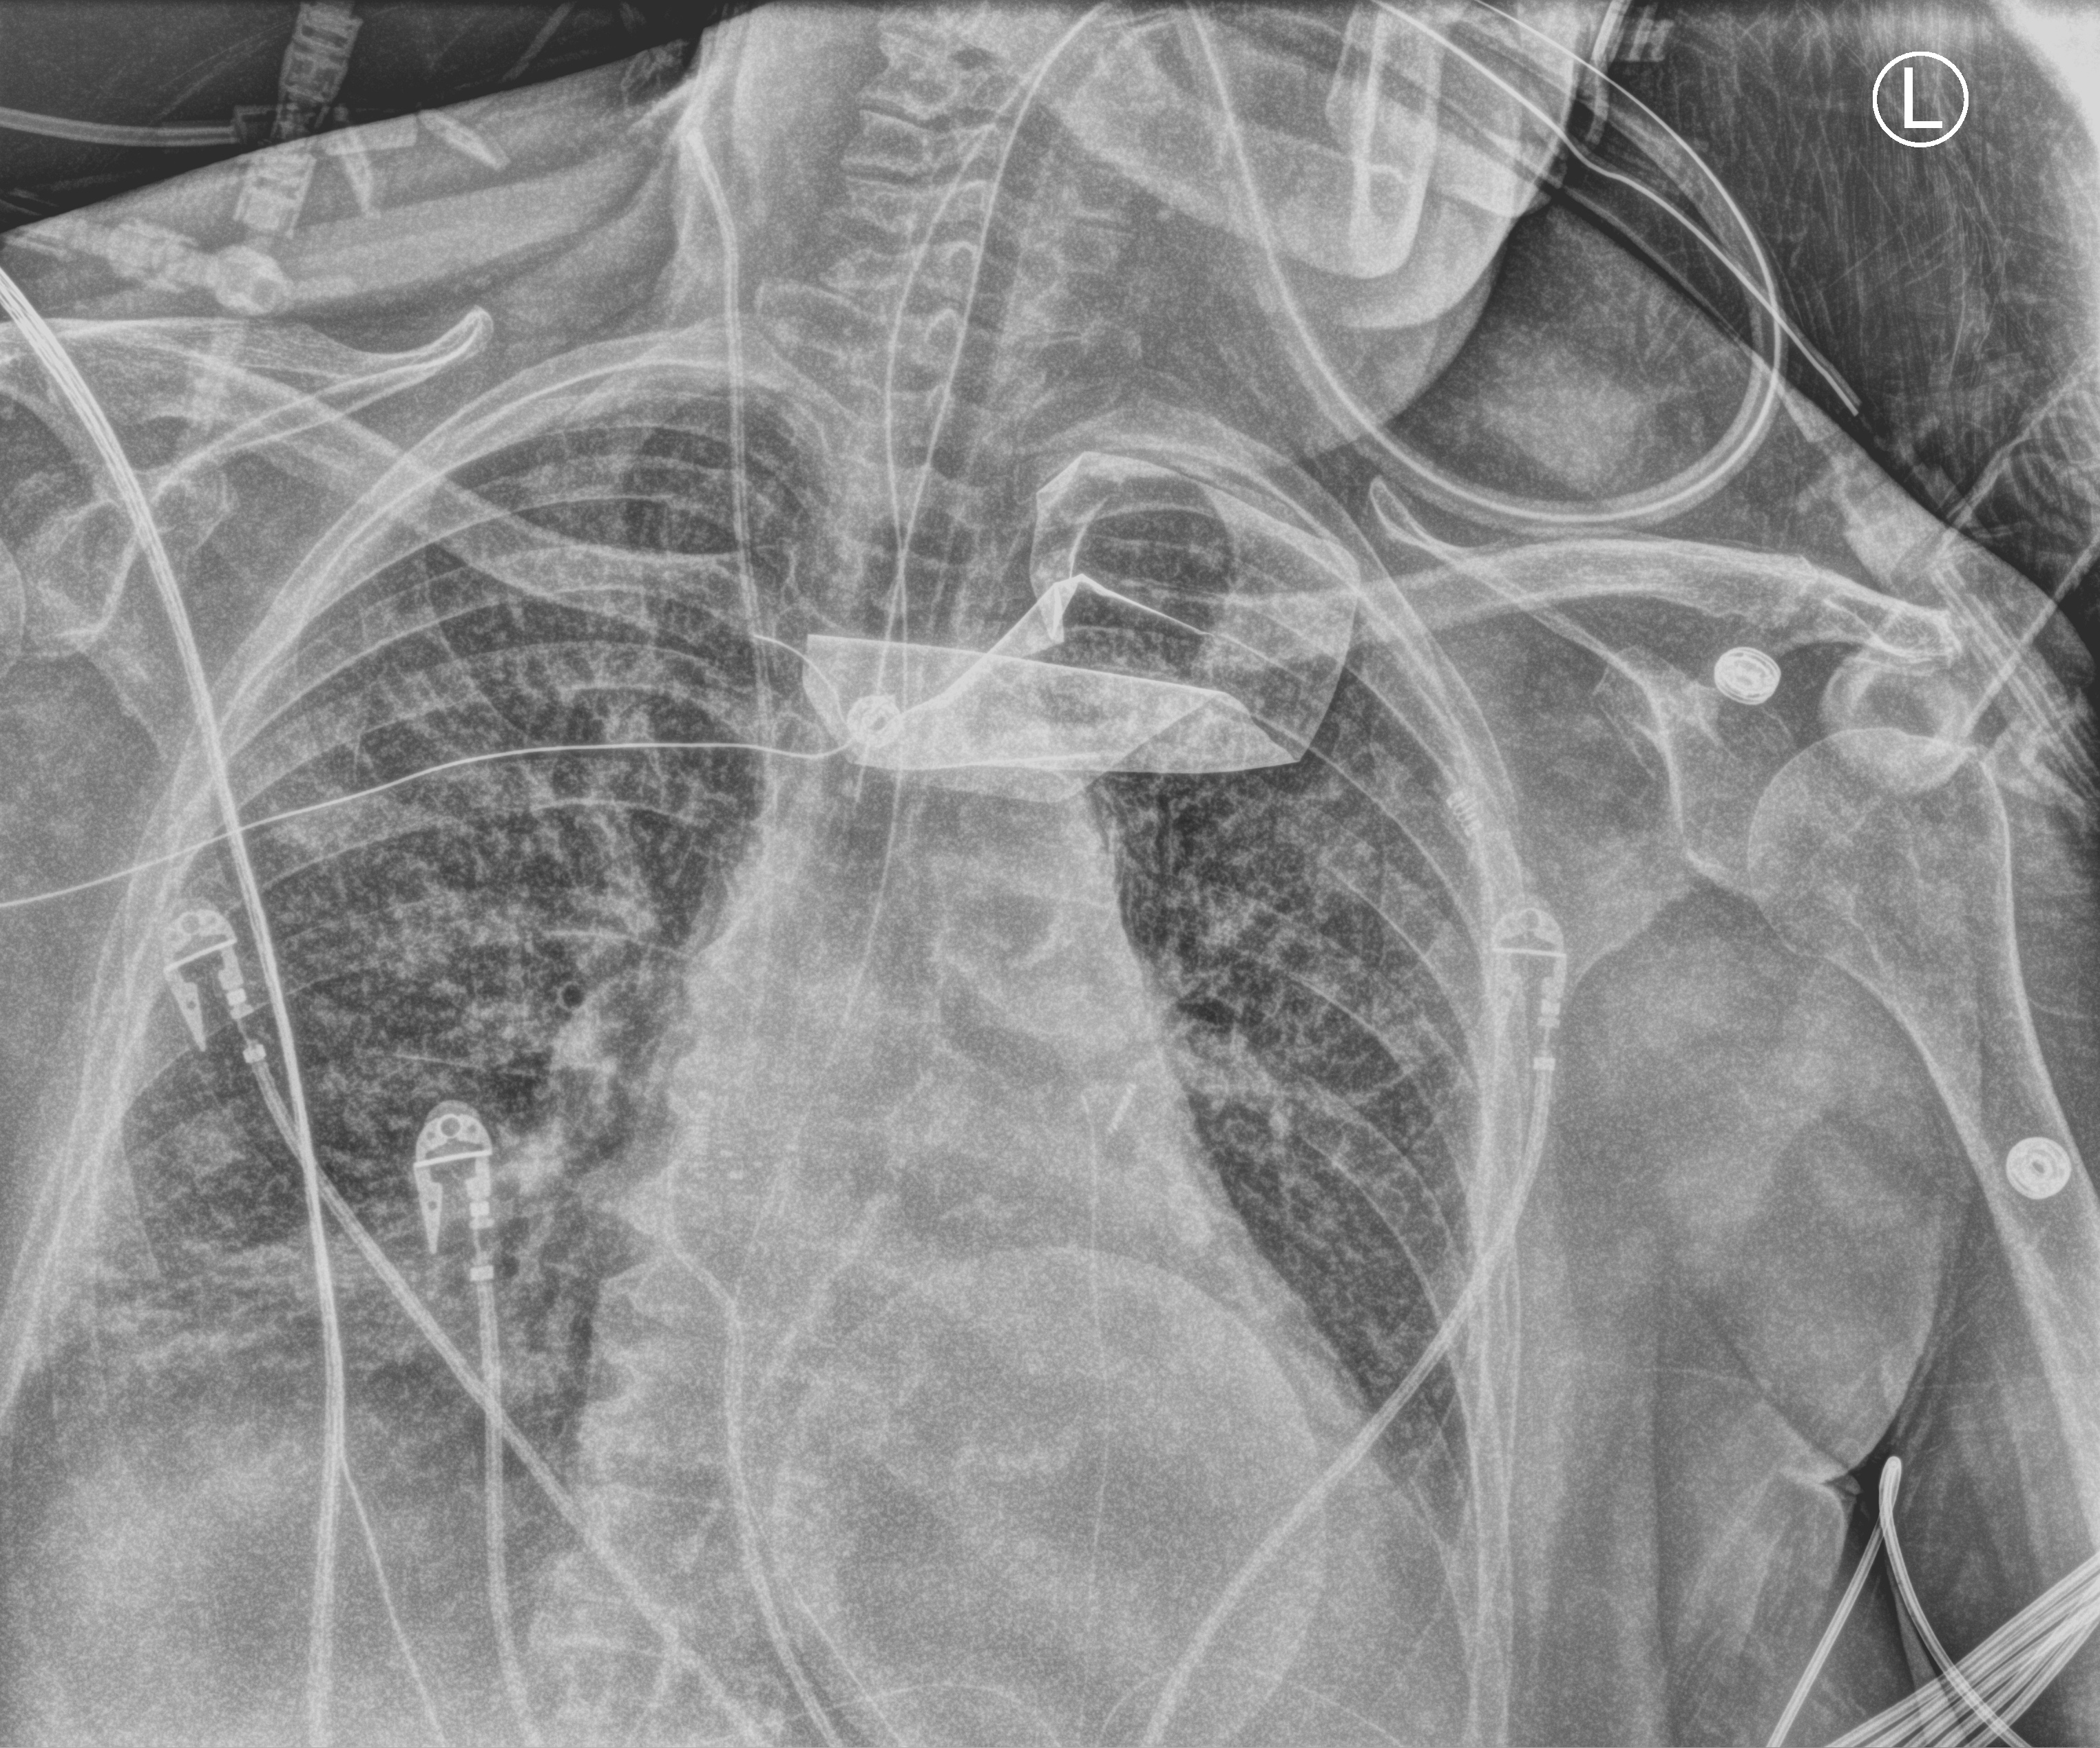
Chest X-ray (portable); anteroposterior (AP) projection. Female patient hospitalised with COVID-19, age 75–90 years.
Hospital-stay facts (about this admission, not read from this image; timing relative to this image not recorded):
- admitted to intensive care during this hospital stay: yes
- mechanically ventilated during this hospital stay: yes